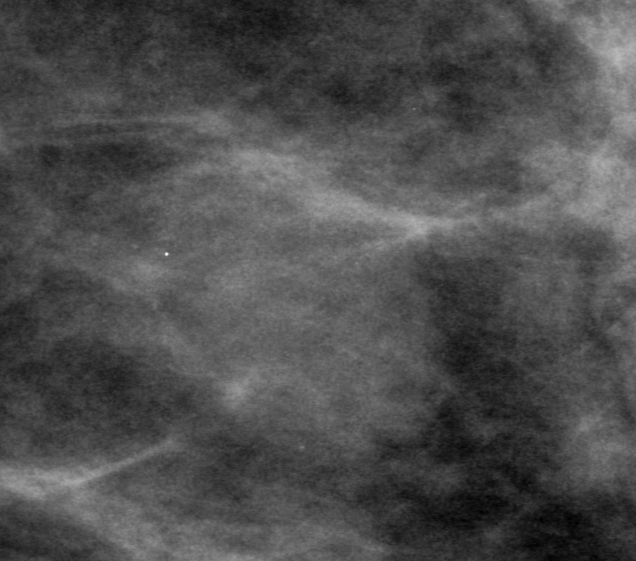
Region of interest cut from a scanned film mammogram (one marked finding); left breast; MLO view.
Marked abnormality: mass, shape oval, margins obscured; BI-RADS assessment category 0 (incomplete: needs additional imaging); subtlety rating 4 on a 1 (subtle) to 5 (obvious) scale; pathology result (as recorded, not read from the image): benign.